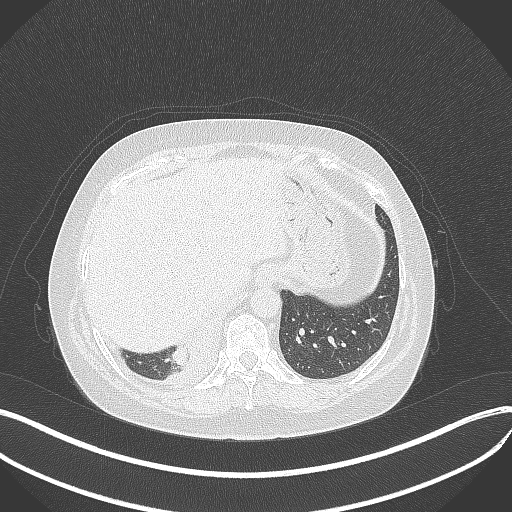
Chest CT, one axial slice. Position 74 of 381 along the scan axis. Reconstruction kernel B70f. Lung window (W 1500 / L -600 HU). 1 mm slice thickness. 512 × 512 image matrix. Female patient, age 56 years. From the clinical record (not read from this slice): clinical TNM (as recorded): T2b N1 M0.
Structures marked on this image (rectangle marked by the reading radiologist):
- lung tumour (recorded histology: small cell carcinoma): bounding box <170,336,199,371> (left, top, right, bottom; pixels)